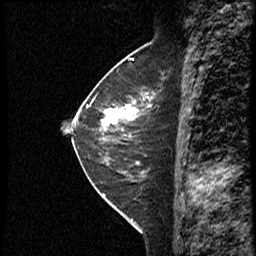
Breast MRI (dynamic contrast-enhanced), one sagittal slice; dynamic contrast-enhanced study with each time point stored as its own series, time point 2 of 4 at this slice position (early post-contrast, ordered by acquisition time); 1.5 T; TE 4.2 ms, TR 18.8 ms; 3 mm slice thickness; 256 × 256 image matrix, field of view 200 × 200 mm. Female patient. From the clinical record (not read from this slice): setting: breast cancer imaged before/during neoadjuvant chemotherapy; receptor status: HER2-positive.
Annotated regions visible in this slice (semi-automatically segmented with operator editing):
- analysis volume of interest (the breast-tissue region the enhancement analysis was run in; not a lesion): bounding box [x1, y1, x2, y2] px = [91, 79, 165, 153]
- tumour enhancement mask (voxels above the 100 % enhancement threshold inside the analysis volume of interest): [102, 98, 150, 126]